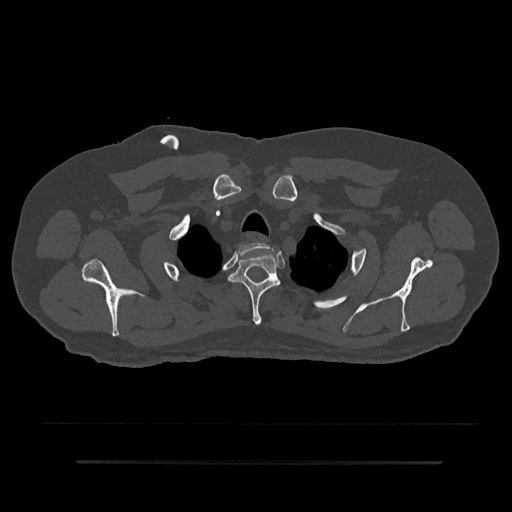
CT including the spine, one axial slice; slice 699 of 797 in the series (ordered by position); reconstruction kernel Br40s/3; 120 kVp; bone window (W 1800 / L 400 HU); 0.5 mm slice thickness; 512 × 512 image matrix. Male patient, age 59 years. Case-level facts recorded for this patient, not image findings: primary cancer: bile ducts.
Annotated regions visible in this slice (semi-automatic segmentation, software-assisted and operator-edited):
- T1 vertebra: bounding box (x1, y1, x2, y2) in pixels: (238, 243, 271, 254)
- T2 vertebra: (228, 253, 281, 325)